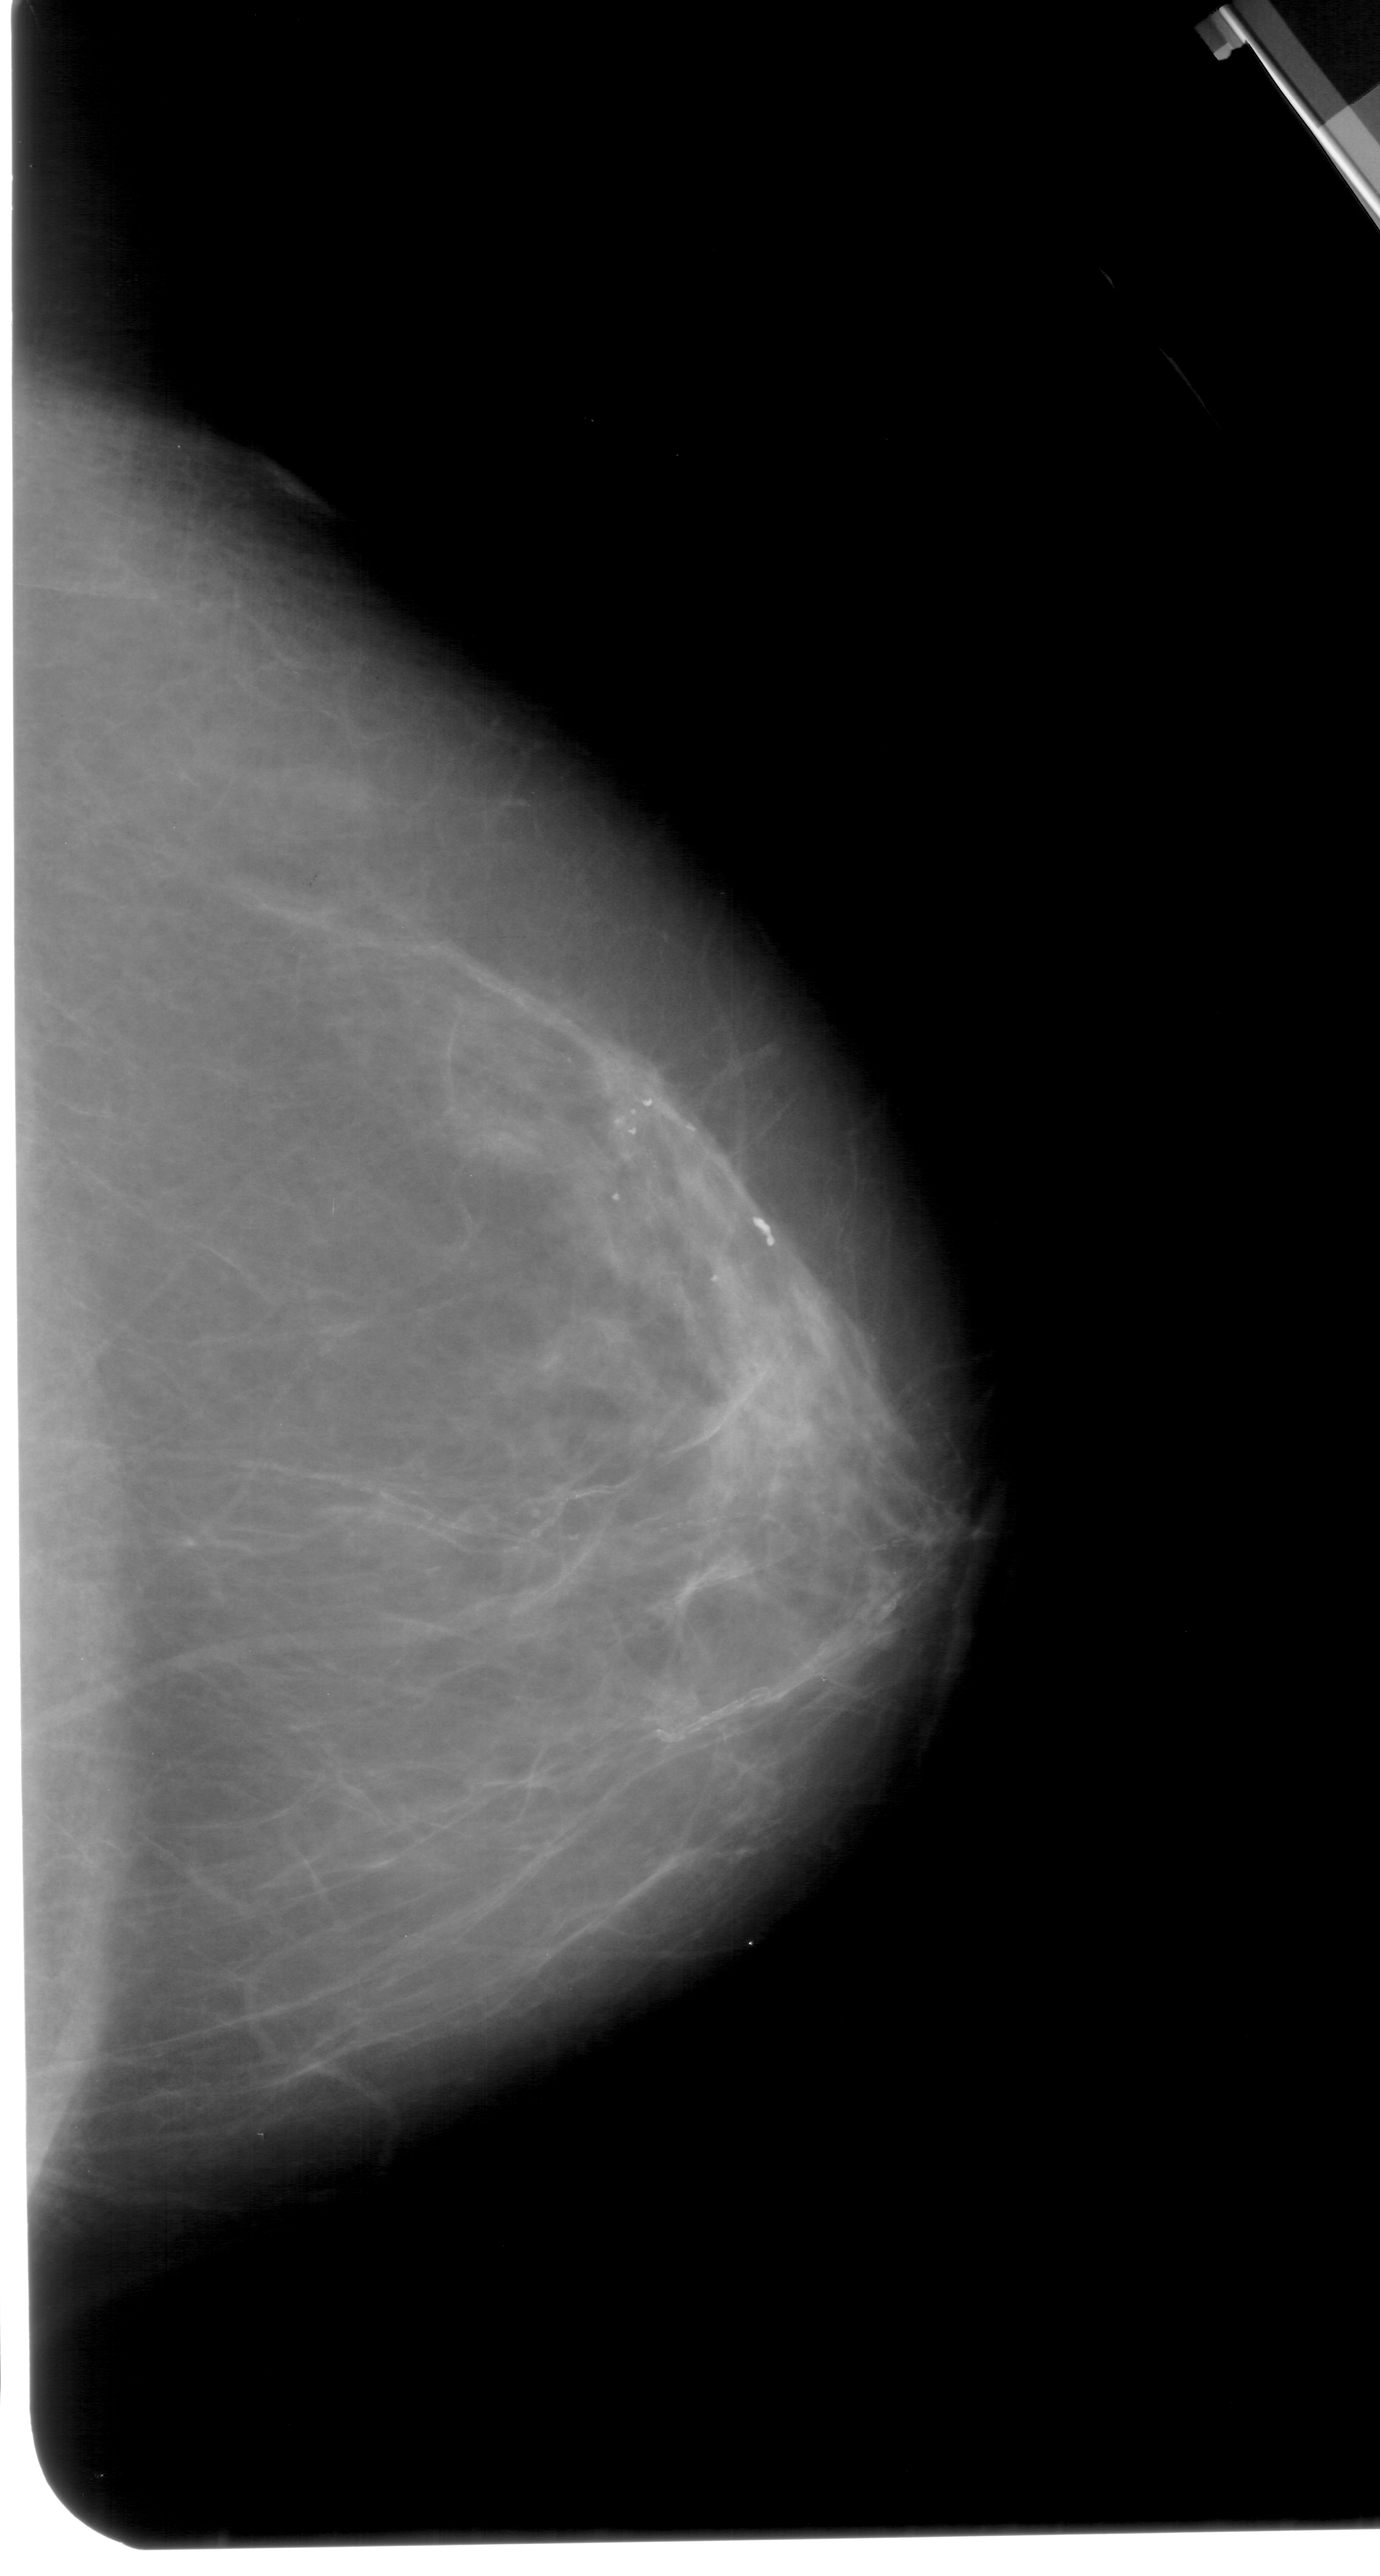
Digitized screen-film mammogram. Right breast. Craniocaudal (CC) view. BI-RADS breast density category 2 (scale 1–4). 1380 × 2576 image matrix.
Expert-marked regions of interest on this film, with their recorded descriptors:
- calcifications, morphology pleomorphic, distribution linear; BI-RADS assessment category 4; pathology result (as recorded, not read from the image): malignant: box from (x=416, y=925) to (x=774, y=1321) px